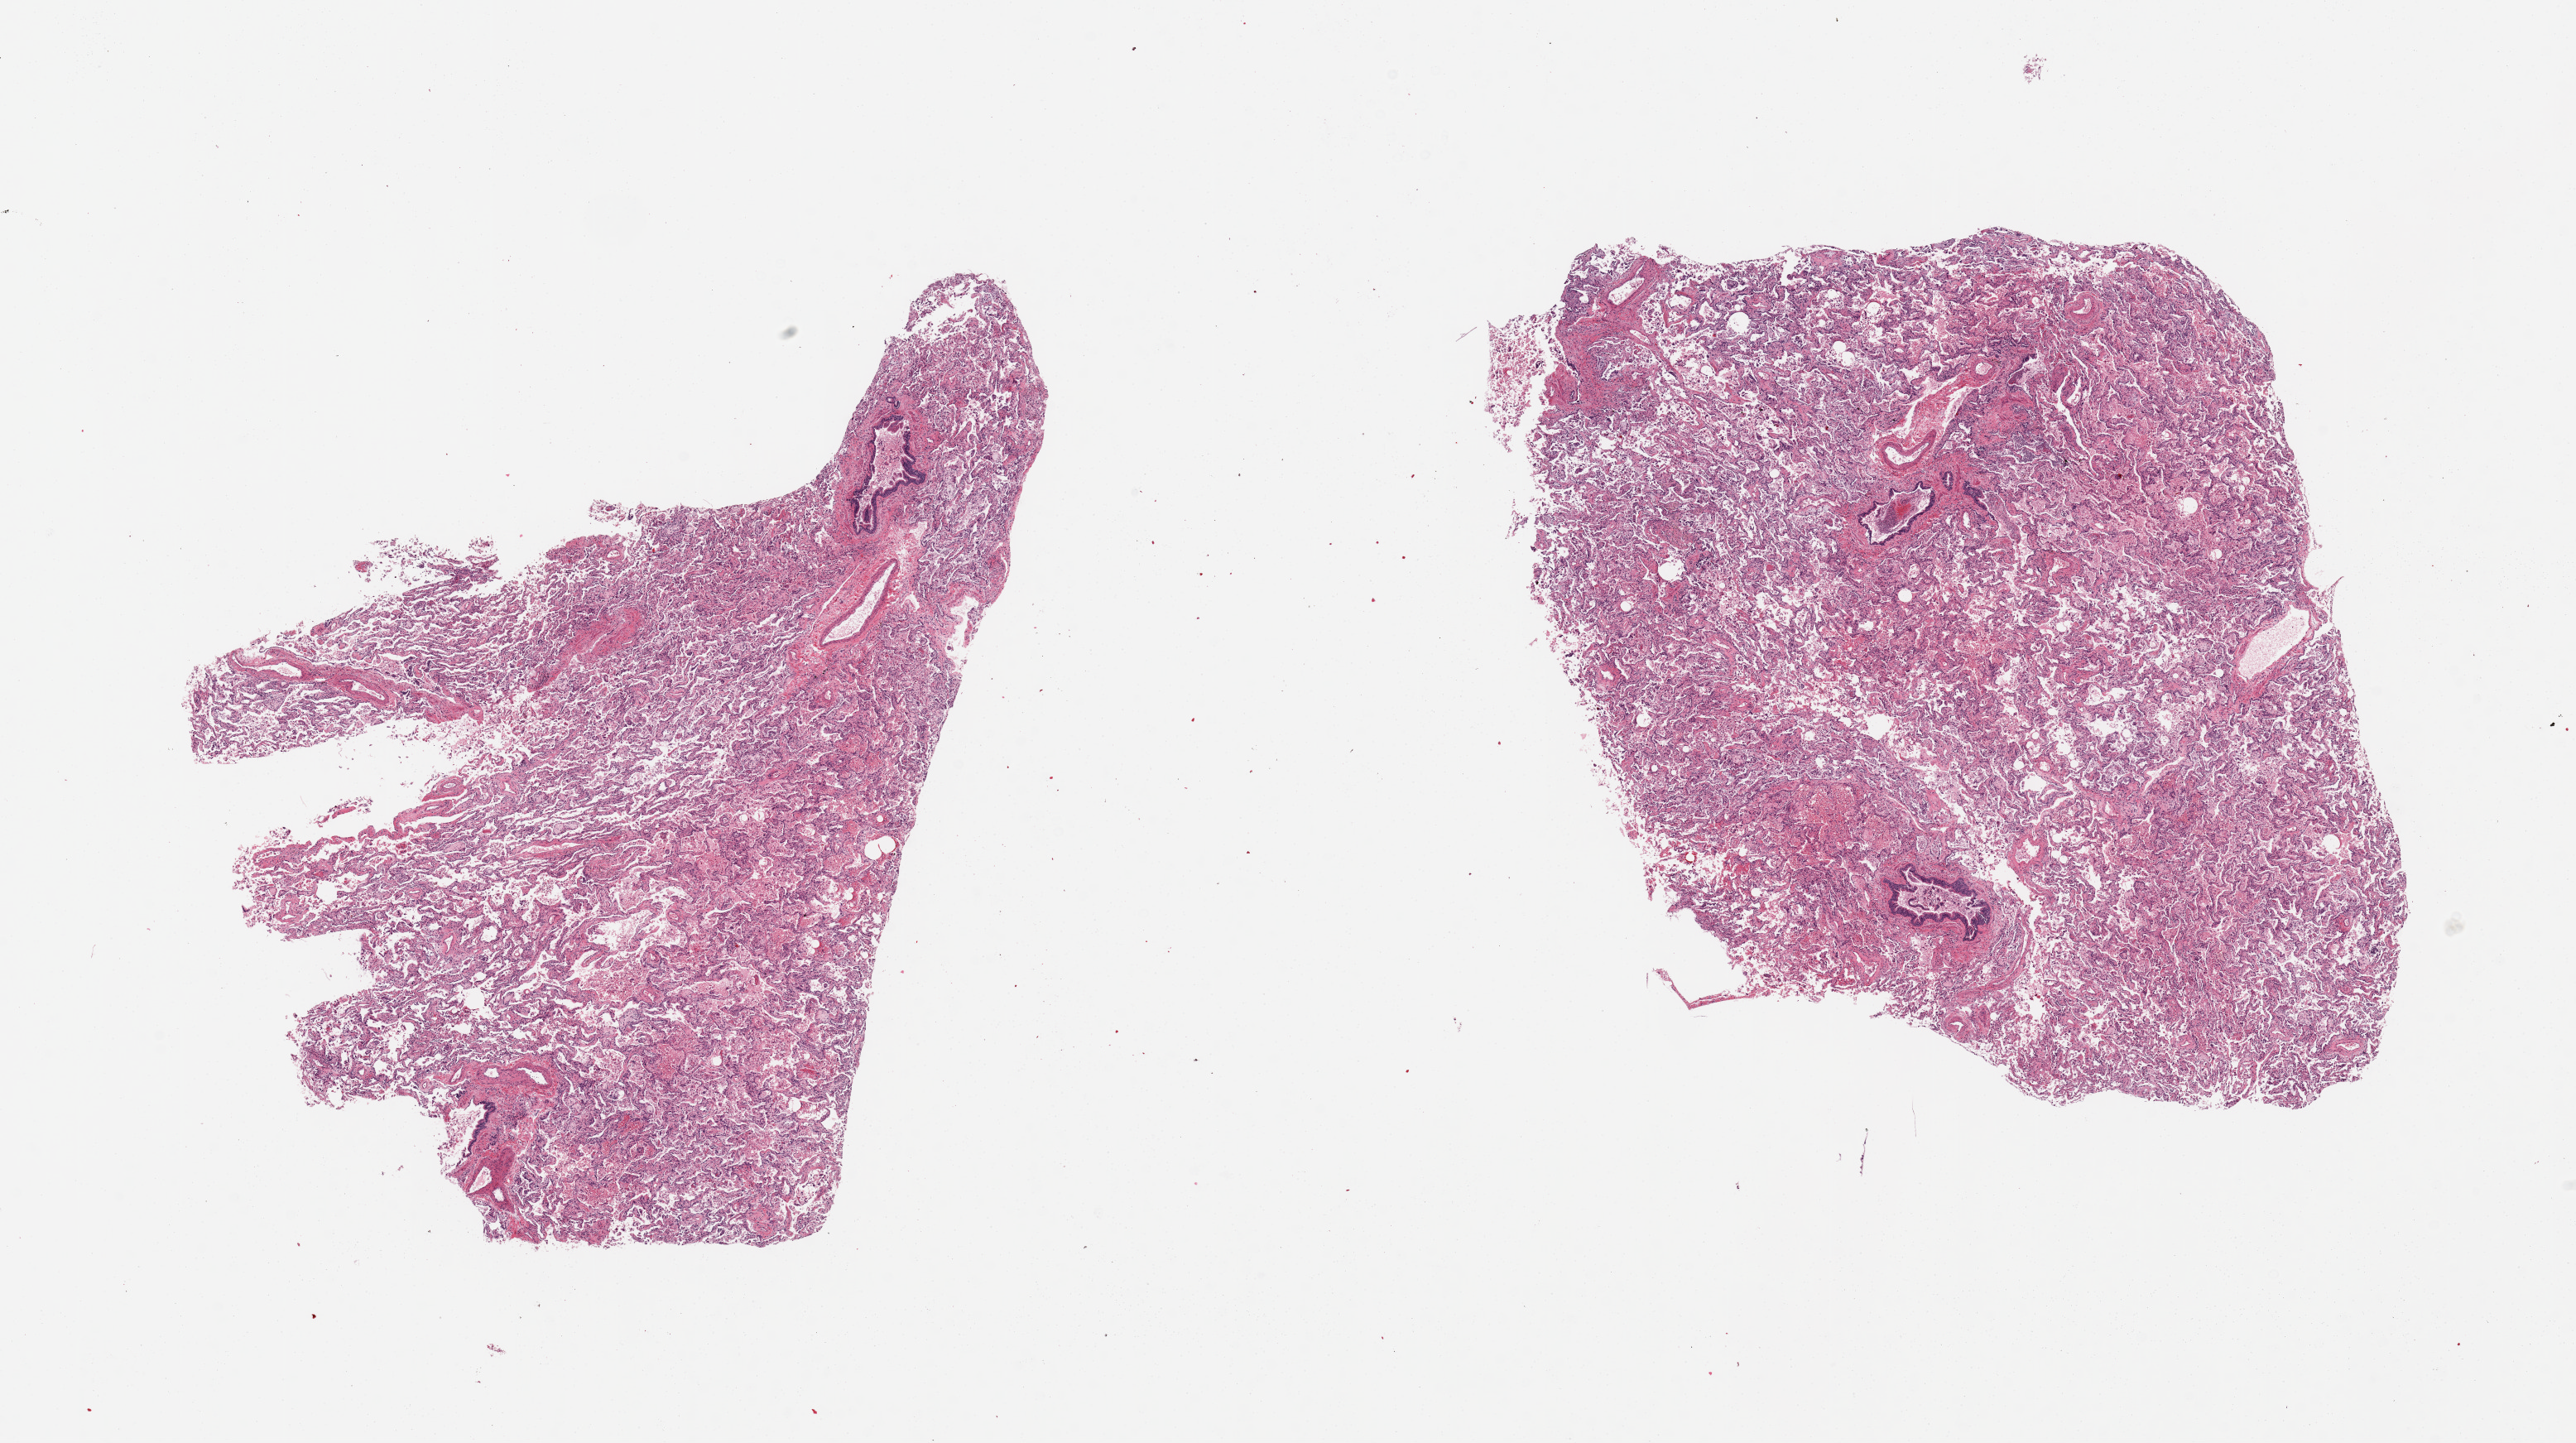
Digitized haematoxylin and eosin-stained section, a low-resolution overview of the entire scanned area, about 24.6 x 13.8 mm (from a 20x scan), PAXgene-fixed paraffin-embedded (PFPE) section, sampled site (target tissue): lung, tissue donor sample.
* review note (as recorded): 2 pieces; moderate interstitial fibrosis